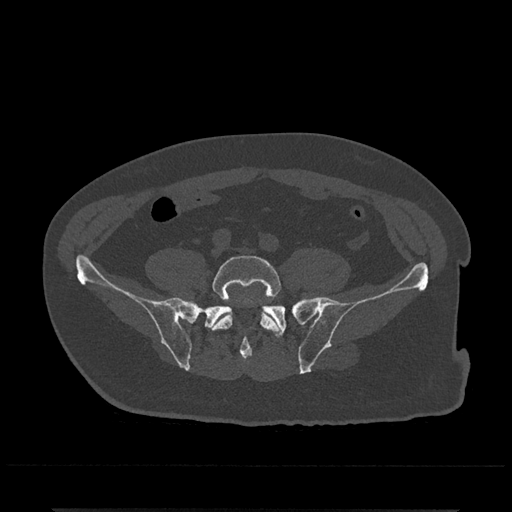
CT including the spine, one axial slice. Slice 62 of 797 in the series (ordered by position). Reconstruction kernel Br40s/3. 120 kVp. Bone window (W 1800 / L 400 HU). 0.5 mm slice thickness. 512 × 512 image matrix, field of view 393 × 393 mm. Patient: male, 67 years. From the clinical record (not read from this slice): primary cancer: prostate.
Annotated regions visible in this slice (semi-automatic segmentation, software-assisted and operator-edited):
- L5 vertebra: bounding box (x1, y1, x2, y2) in pixels: (210, 255, 280, 333)